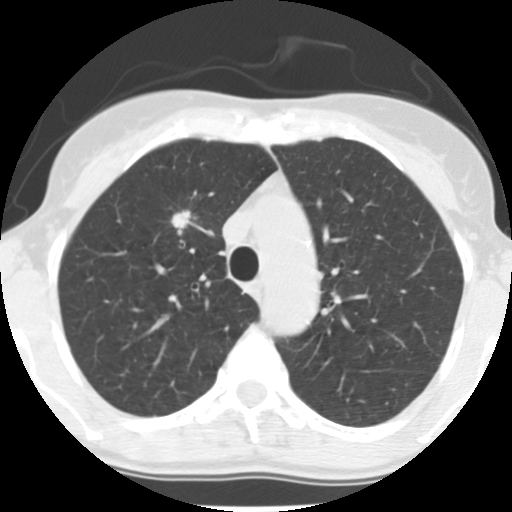
Chest CT (low-dose screening protocol), one axial image; second screening round (one year after baseline); lung window (W 1500 / L -600 HU); 2.5 mm slice thickness; 512 × 512 image matrix, field of view 280 × 280 mm. Female participant, aged 56 years at enrolment. Former smoker at enrolment.
• Lesion marked by an expert reader, box from (x=157, y=202) to (x=200, y=245) px.
• Reader record for this screening exam (exam-level; its link to the box is not recorded): non-calcified nodule or mass ≥4 mm, right upper lobe, 12 × 9 mm, spiculated (stellate) margins, soft tissue attenuation, pre-existing on the prior screen: yes; interval growth: no.
• Later outcome: lung cancer diagnosed 350 days after this screen (after the third annual screen) — adenocarcinoma, NOS, right upper lobe, moderately differentiated (G2), stage IA (AJCC 6th edition), 19 mm at pathology.